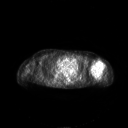
FDG PET of an extremity soft-tissue mass (from a PET/CT study), one axial slice. 3.27 mm slice thickness. 128 × 128 image matrix, field of view 700 × 700 mm. Female patient, age 83 years. From the clinical record (not read from this slice): histological type: pleiomorphic leiomyosarcoma; grade: high; site of the primary tumour: left biceps.
Annotated regions visible in this slice (expert contour drawn on MRI and transferred to this co-registered scan by the dataset authors):
- gross tumour volume including surrounding oedema: bounding box <90,59,105,77> (left, top, right, bottom; pixels)
- gross tumour volume (mass): <90,59,104,76>